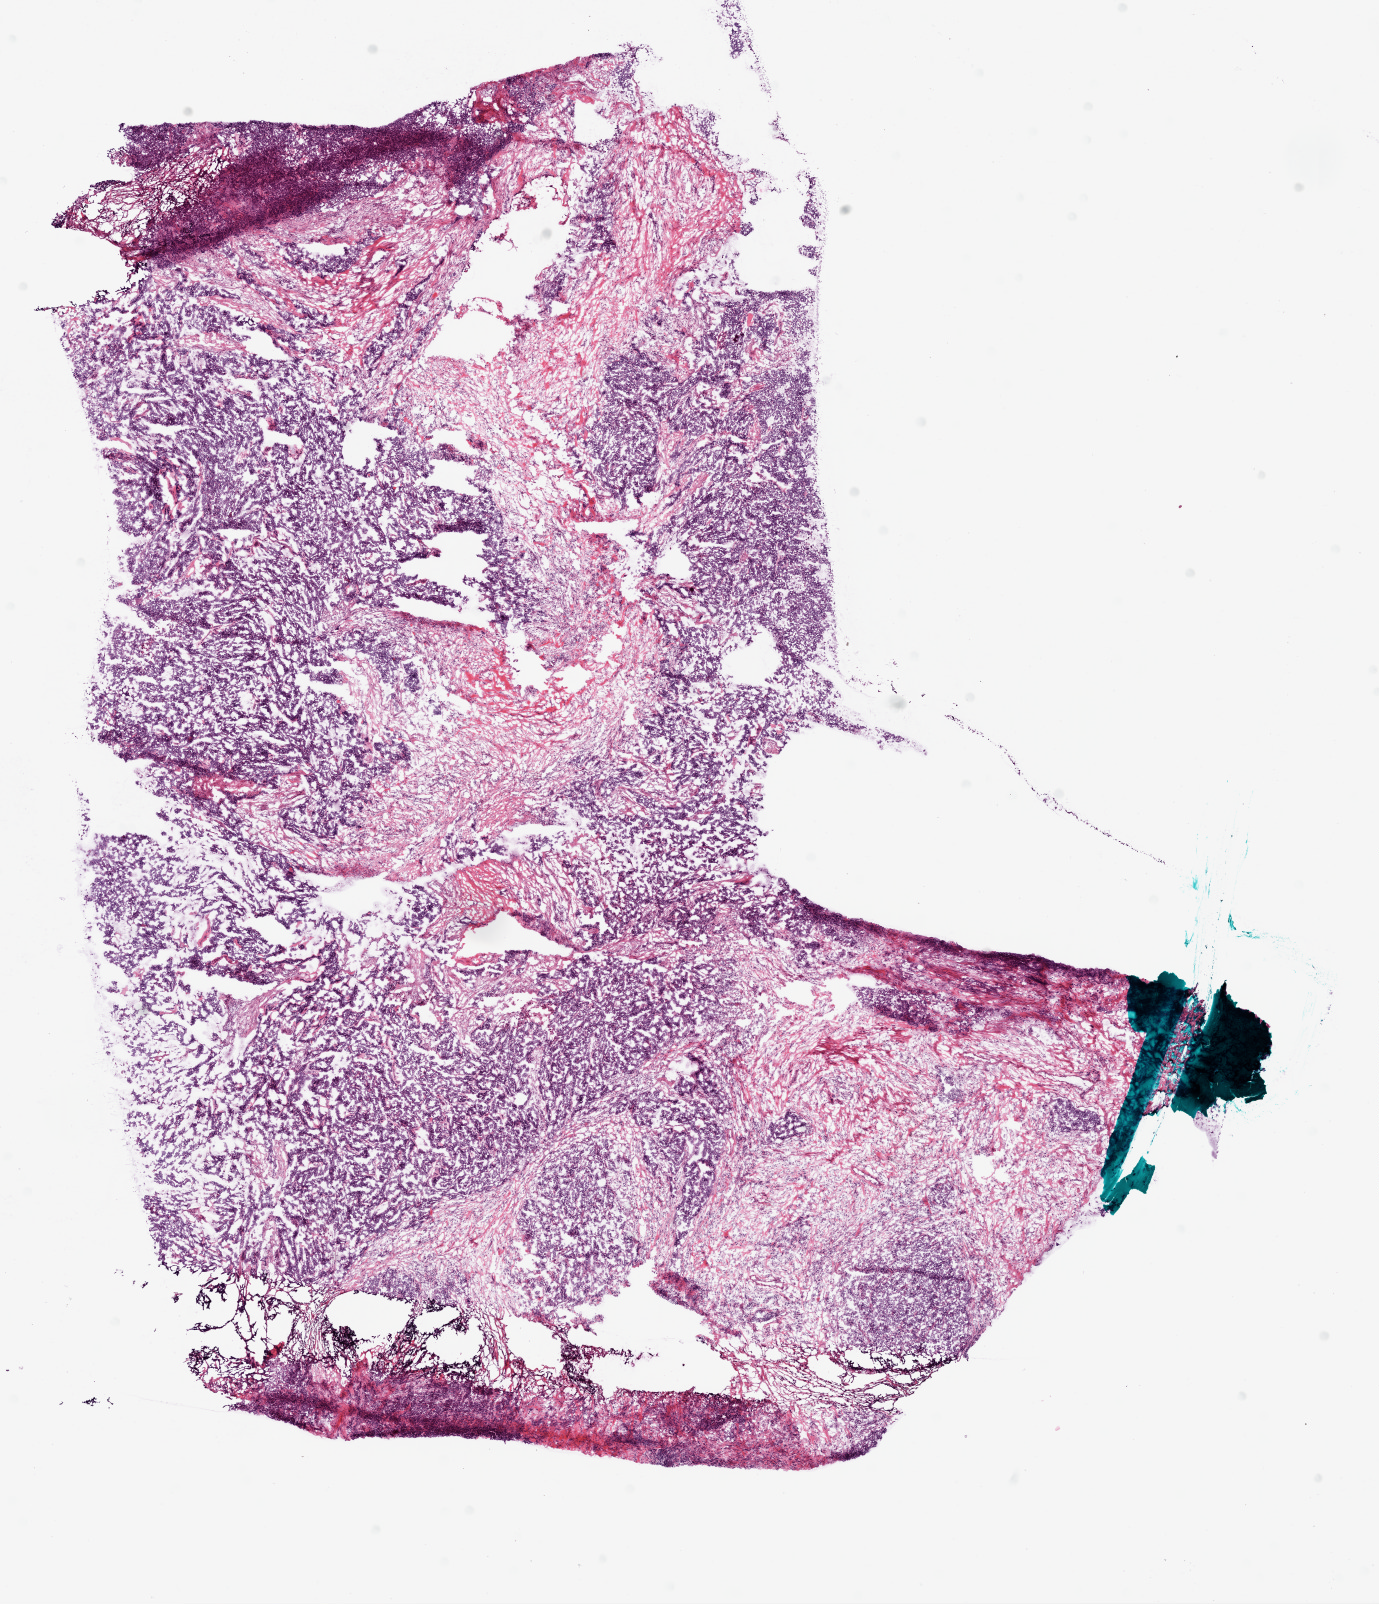
Whole-slide histology image, Hematoxylin and eosin (H&E) stained, shown as a low-resolution overview of the whole scanned area (about 11.1 x 12.9 mm). Frozen section. Sample: primary tumour, ovary. Female, age 81 years at initial diagnosis. Histologic grade: G3 (poorly differentiated). Slide review estimates, as recorded: tumour cells 55%, tumour nuclei 70%, normal cells 0%, stromal cells 40%, necrosis 5%.
Pathologic diagnosis: Serous cystadenocarcinoma, NOS. FIGO stage: IV.